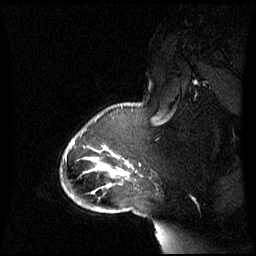
Breast MRI (dynamic contrast-enhanced), one sagittal slice; slice 49 of 60 in the series (ordered by position); dynamic contrast-enhanced series, image 2 of 3 at this slice position (ordered by acquisition); 1.5 T; TE 4.2 ms, TR 8.4 ms; 2.8 mm slice thickness; 256 × 256 image matrix. Female patient, age 43 years. From the clinical record (not read from this slice): setting: breast cancer imaged before/during neoadjuvant chemotherapy; receptor status: triple-negative.
Structures marked on this image (semi-automatic segmentation, software-assisted and operator-edited):
- analysis volume of interest (the breast-tissue region the enhancement analysis was run in; not a lesion): bounding box (x1, y1, x2, y2) in pixels: (65, 118, 143, 198)
- tumour enhancement mask (voxels above the 70 % enhancement threshold inside the analysis volume of interest): (92, 146, 129, 194)